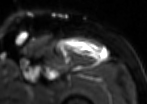
MRI of an extremity soft-tissue mass, one axial slice. Slice 76 of 85 in the series (ordered by position). T2-weighted fat-saturated. MR volume resampled by the dataset authors to the PET/CT grid (not the native acquisition matrix). 3.27 mm slice thickness. 147 × 104 image matrix, field of view 144 × 102 mm. Male patient. From the clinical record (not read from this slice): histological type: extraskeletal osteosarcoma; grade: high; site of the primary tumour: thigh.
Outlined on this slice (expert contour drawn on MRI and transferred to this co-registered scan by the dataset authors):
- gross tumour volume (mass): bounding box (x1, y1, x2, y2) in pixels: (62, 37, 107, 61)